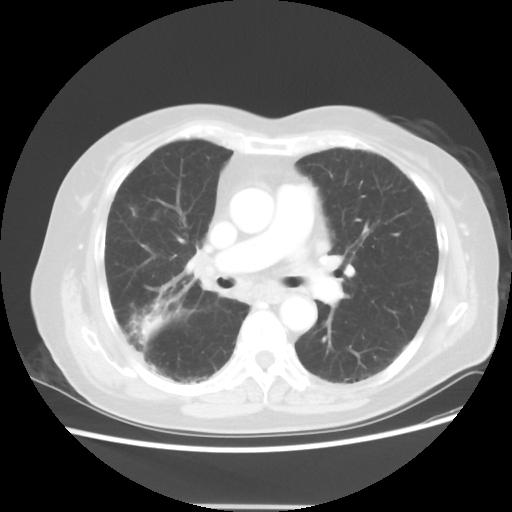
Chest CT, one axial slice; position 27 of 50 along the scan axis; reconstruction kernel STANDARD; 120 kVp; lung window (W 1500 / L -600 HU); 5 mm slice thickness; 512 × 512 image matrix. Female patient, age 72 years. From the clinical record (not read from this slice): clinical TNM (as recorded): T2 N1 M0.
Structures marked on this image (bounding box drawn by a radiologist):
- lung tumour (recorded histology: adenocarcinoma): bounding box <143,313,162,336> (left, top, right, bottom; pixels)